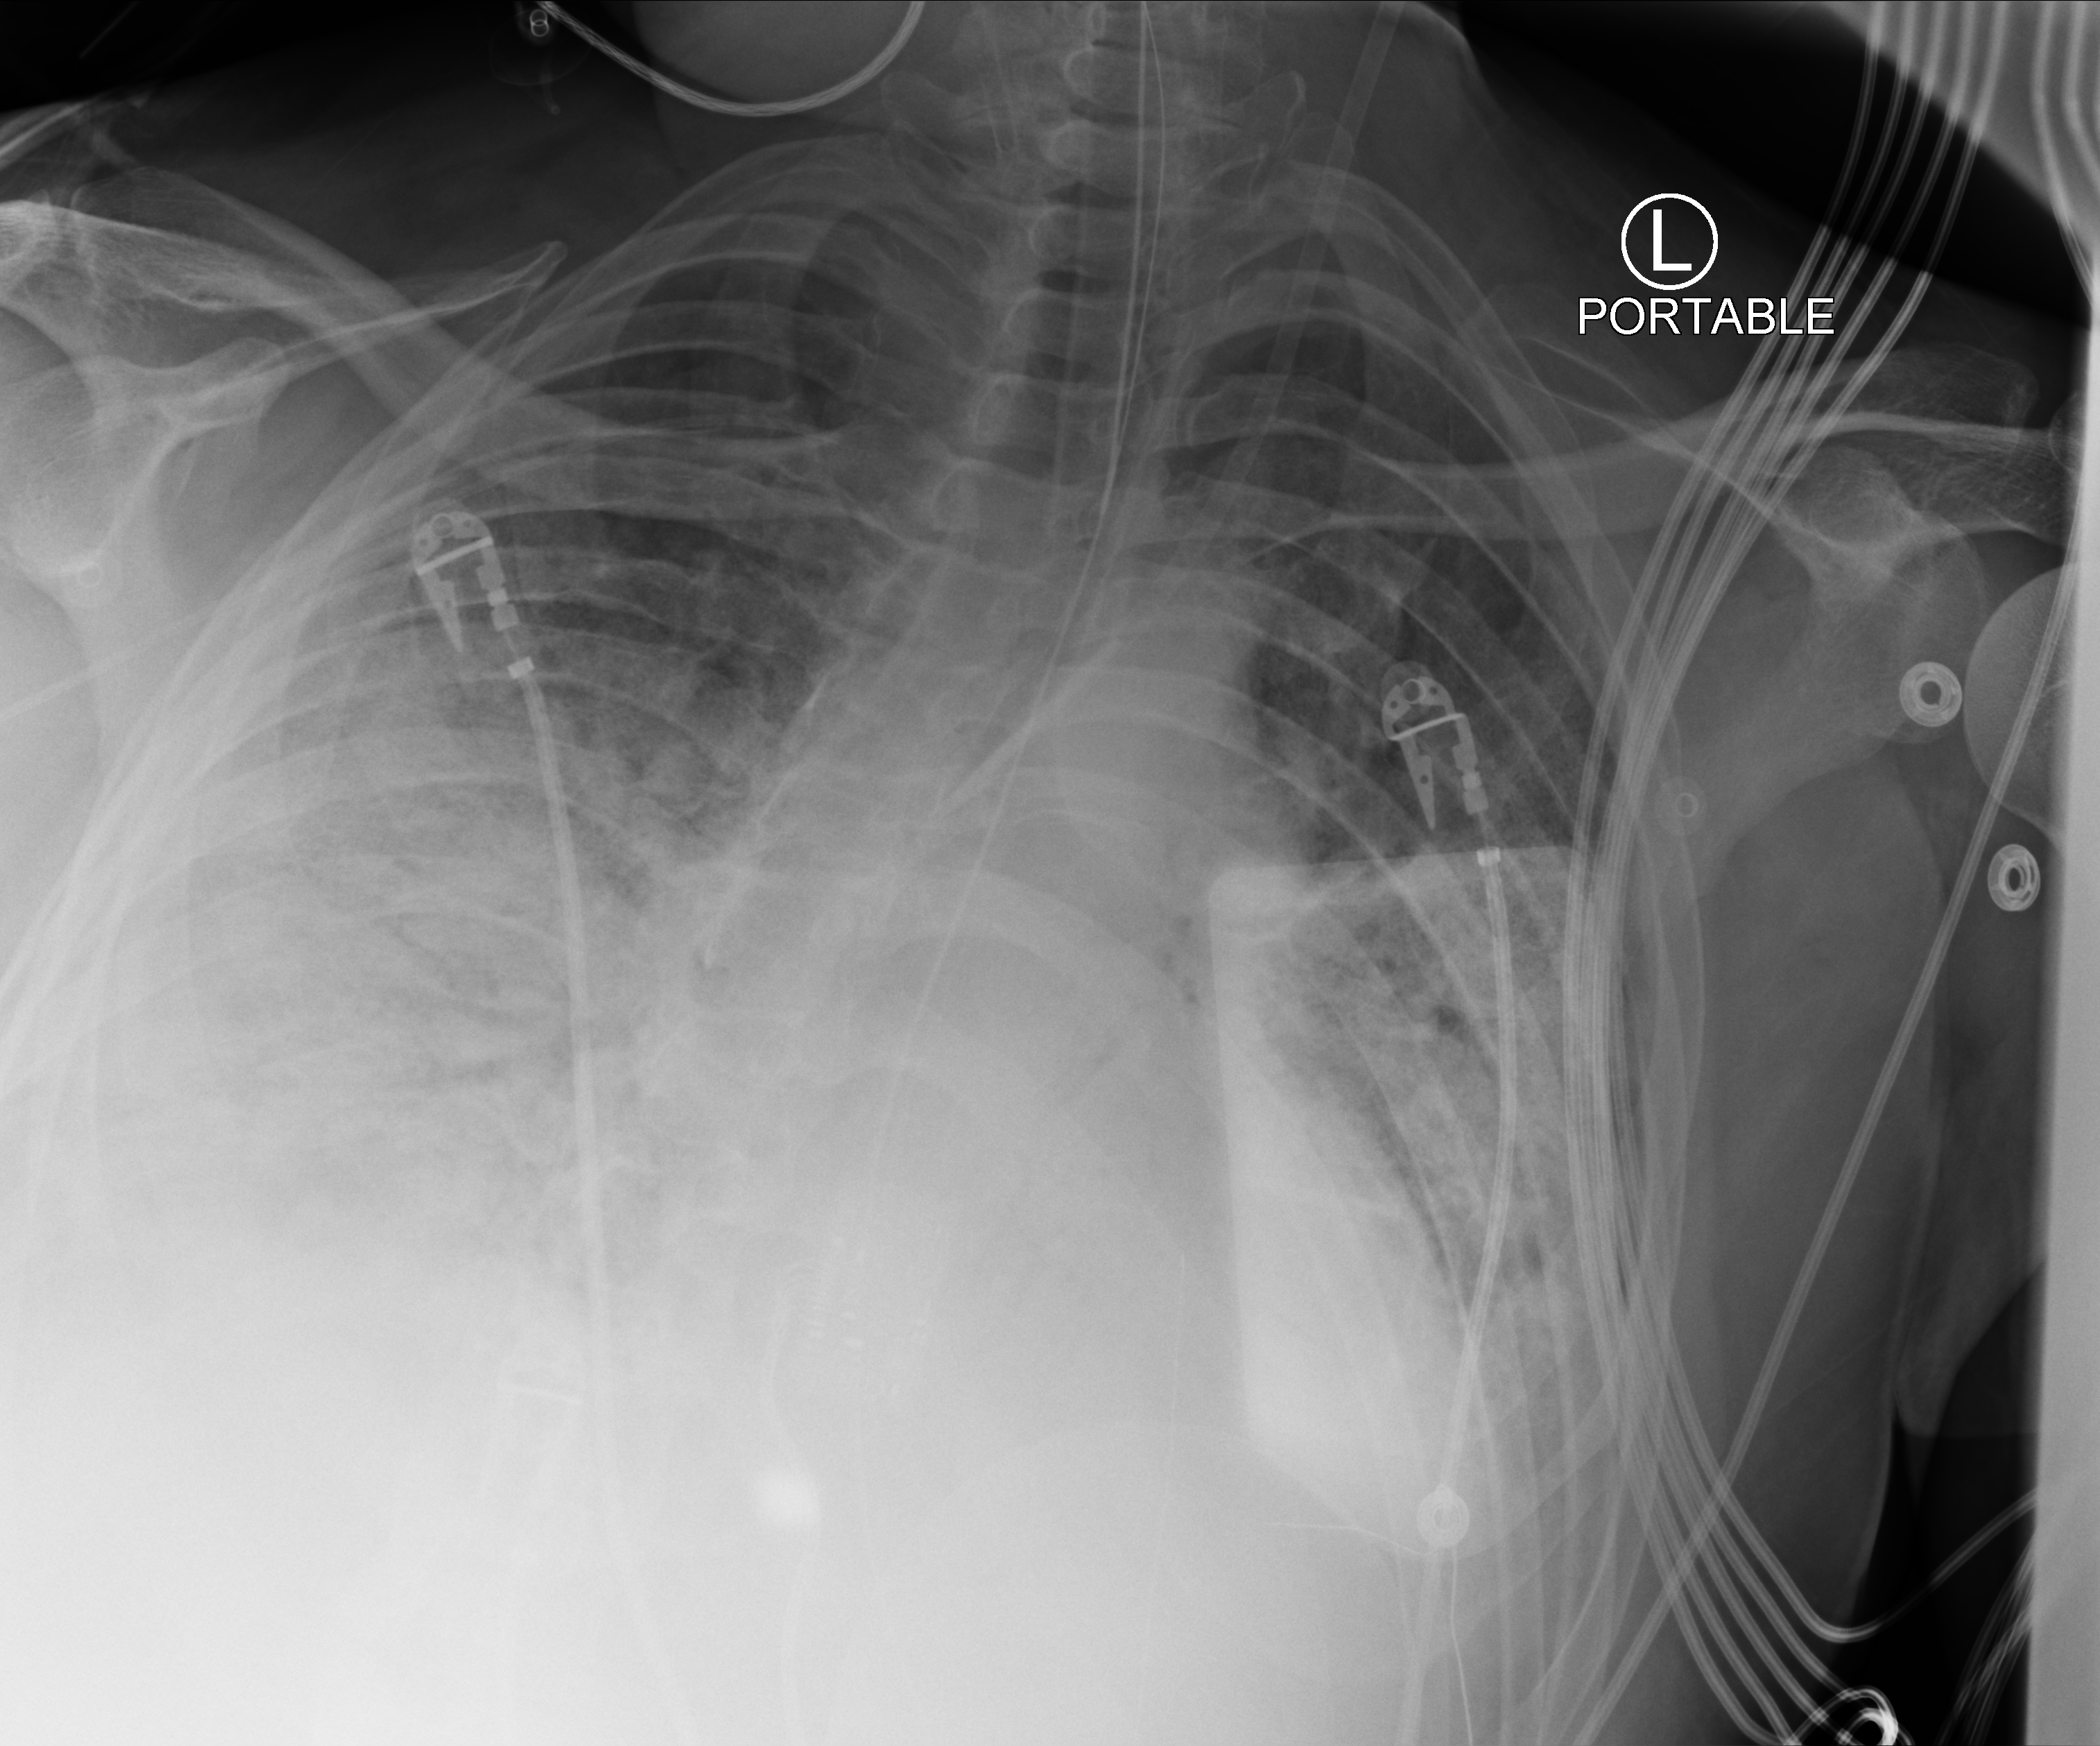
Chest X-ray (portable), anteroposterior (AP) projection. Patient hospitalised with COVID-19; male, aged 18–59 years.
From the hospital-stay record, not from the radiograph (when in the stay this image was taken is not recorded): admitted to intensive care during this hospital stay: yes.